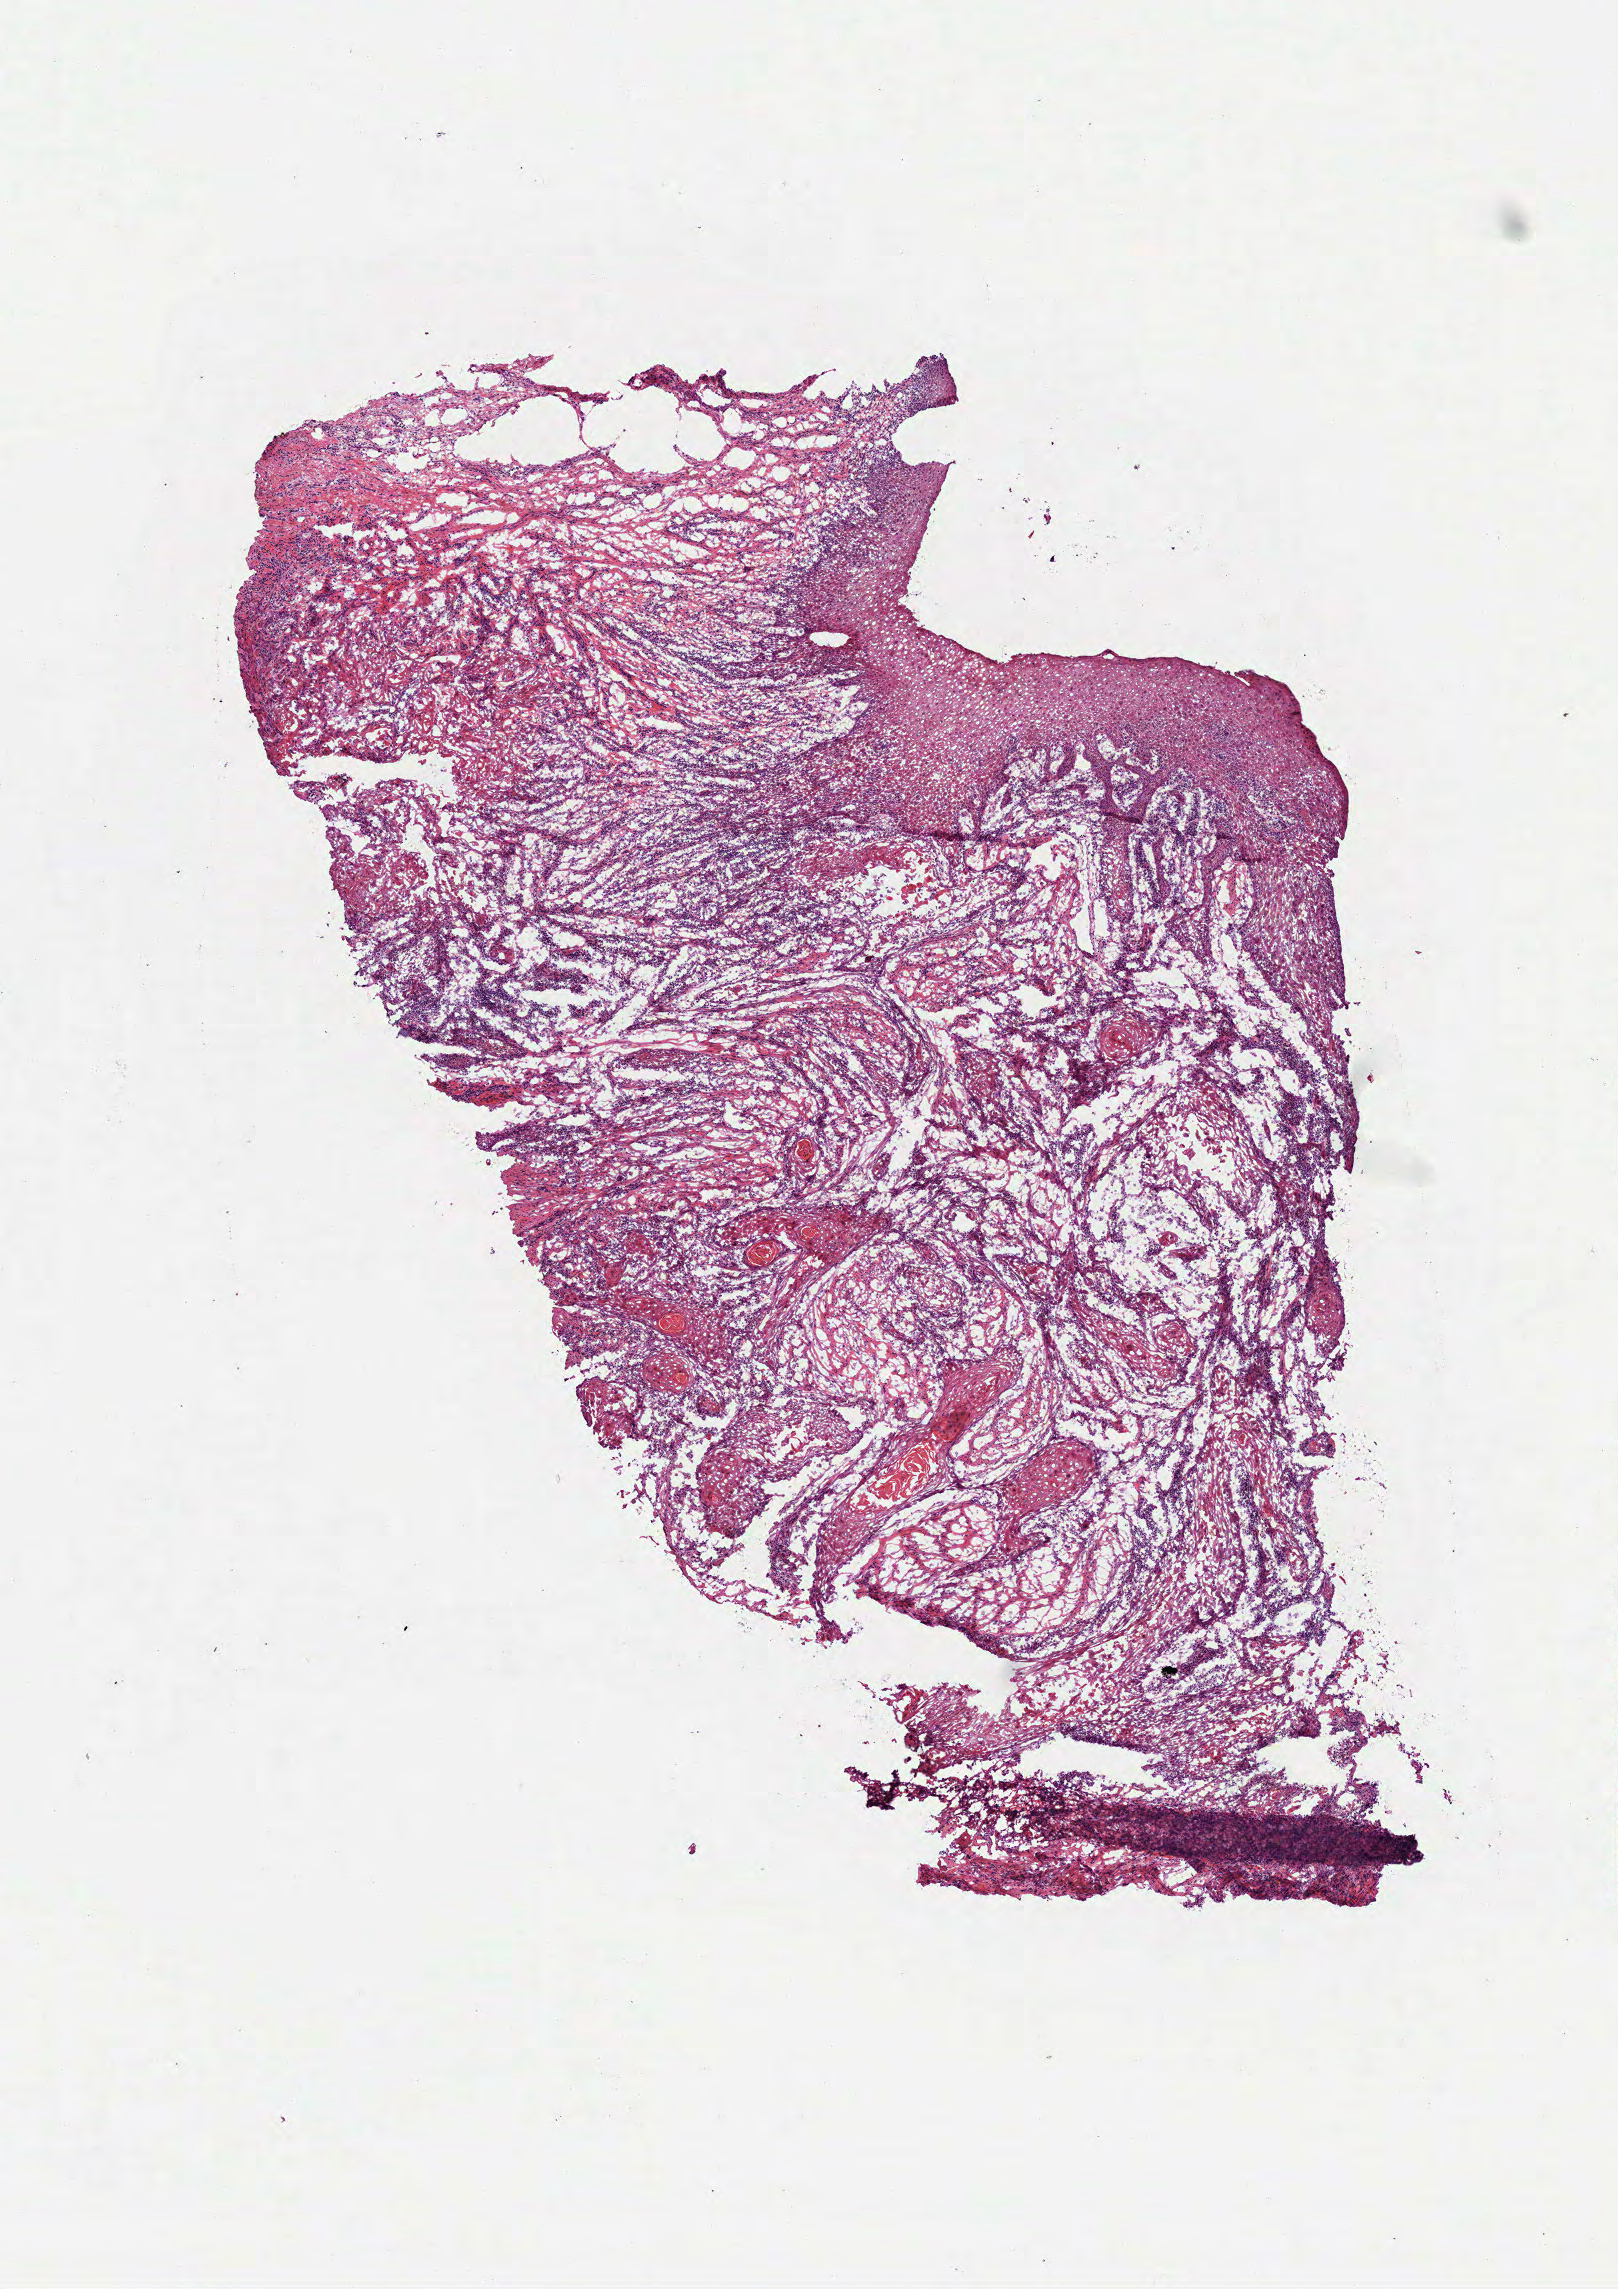
H&E-stained whole-slide image — low-resolution overview of the scanned area, about 6.5 x 9.2 mm (acquisition: 40x scan). Frozen section. Primary tumour sample from the head and neck. Male, age 74 years at initial diagnosis. Pathologist review of this section (percent, as recorded): tumour cells 80%, tumour nuclei 75%.
Histologic diagnosis: Squamous cell carcinoma, NOS (base of tongue, NOS).